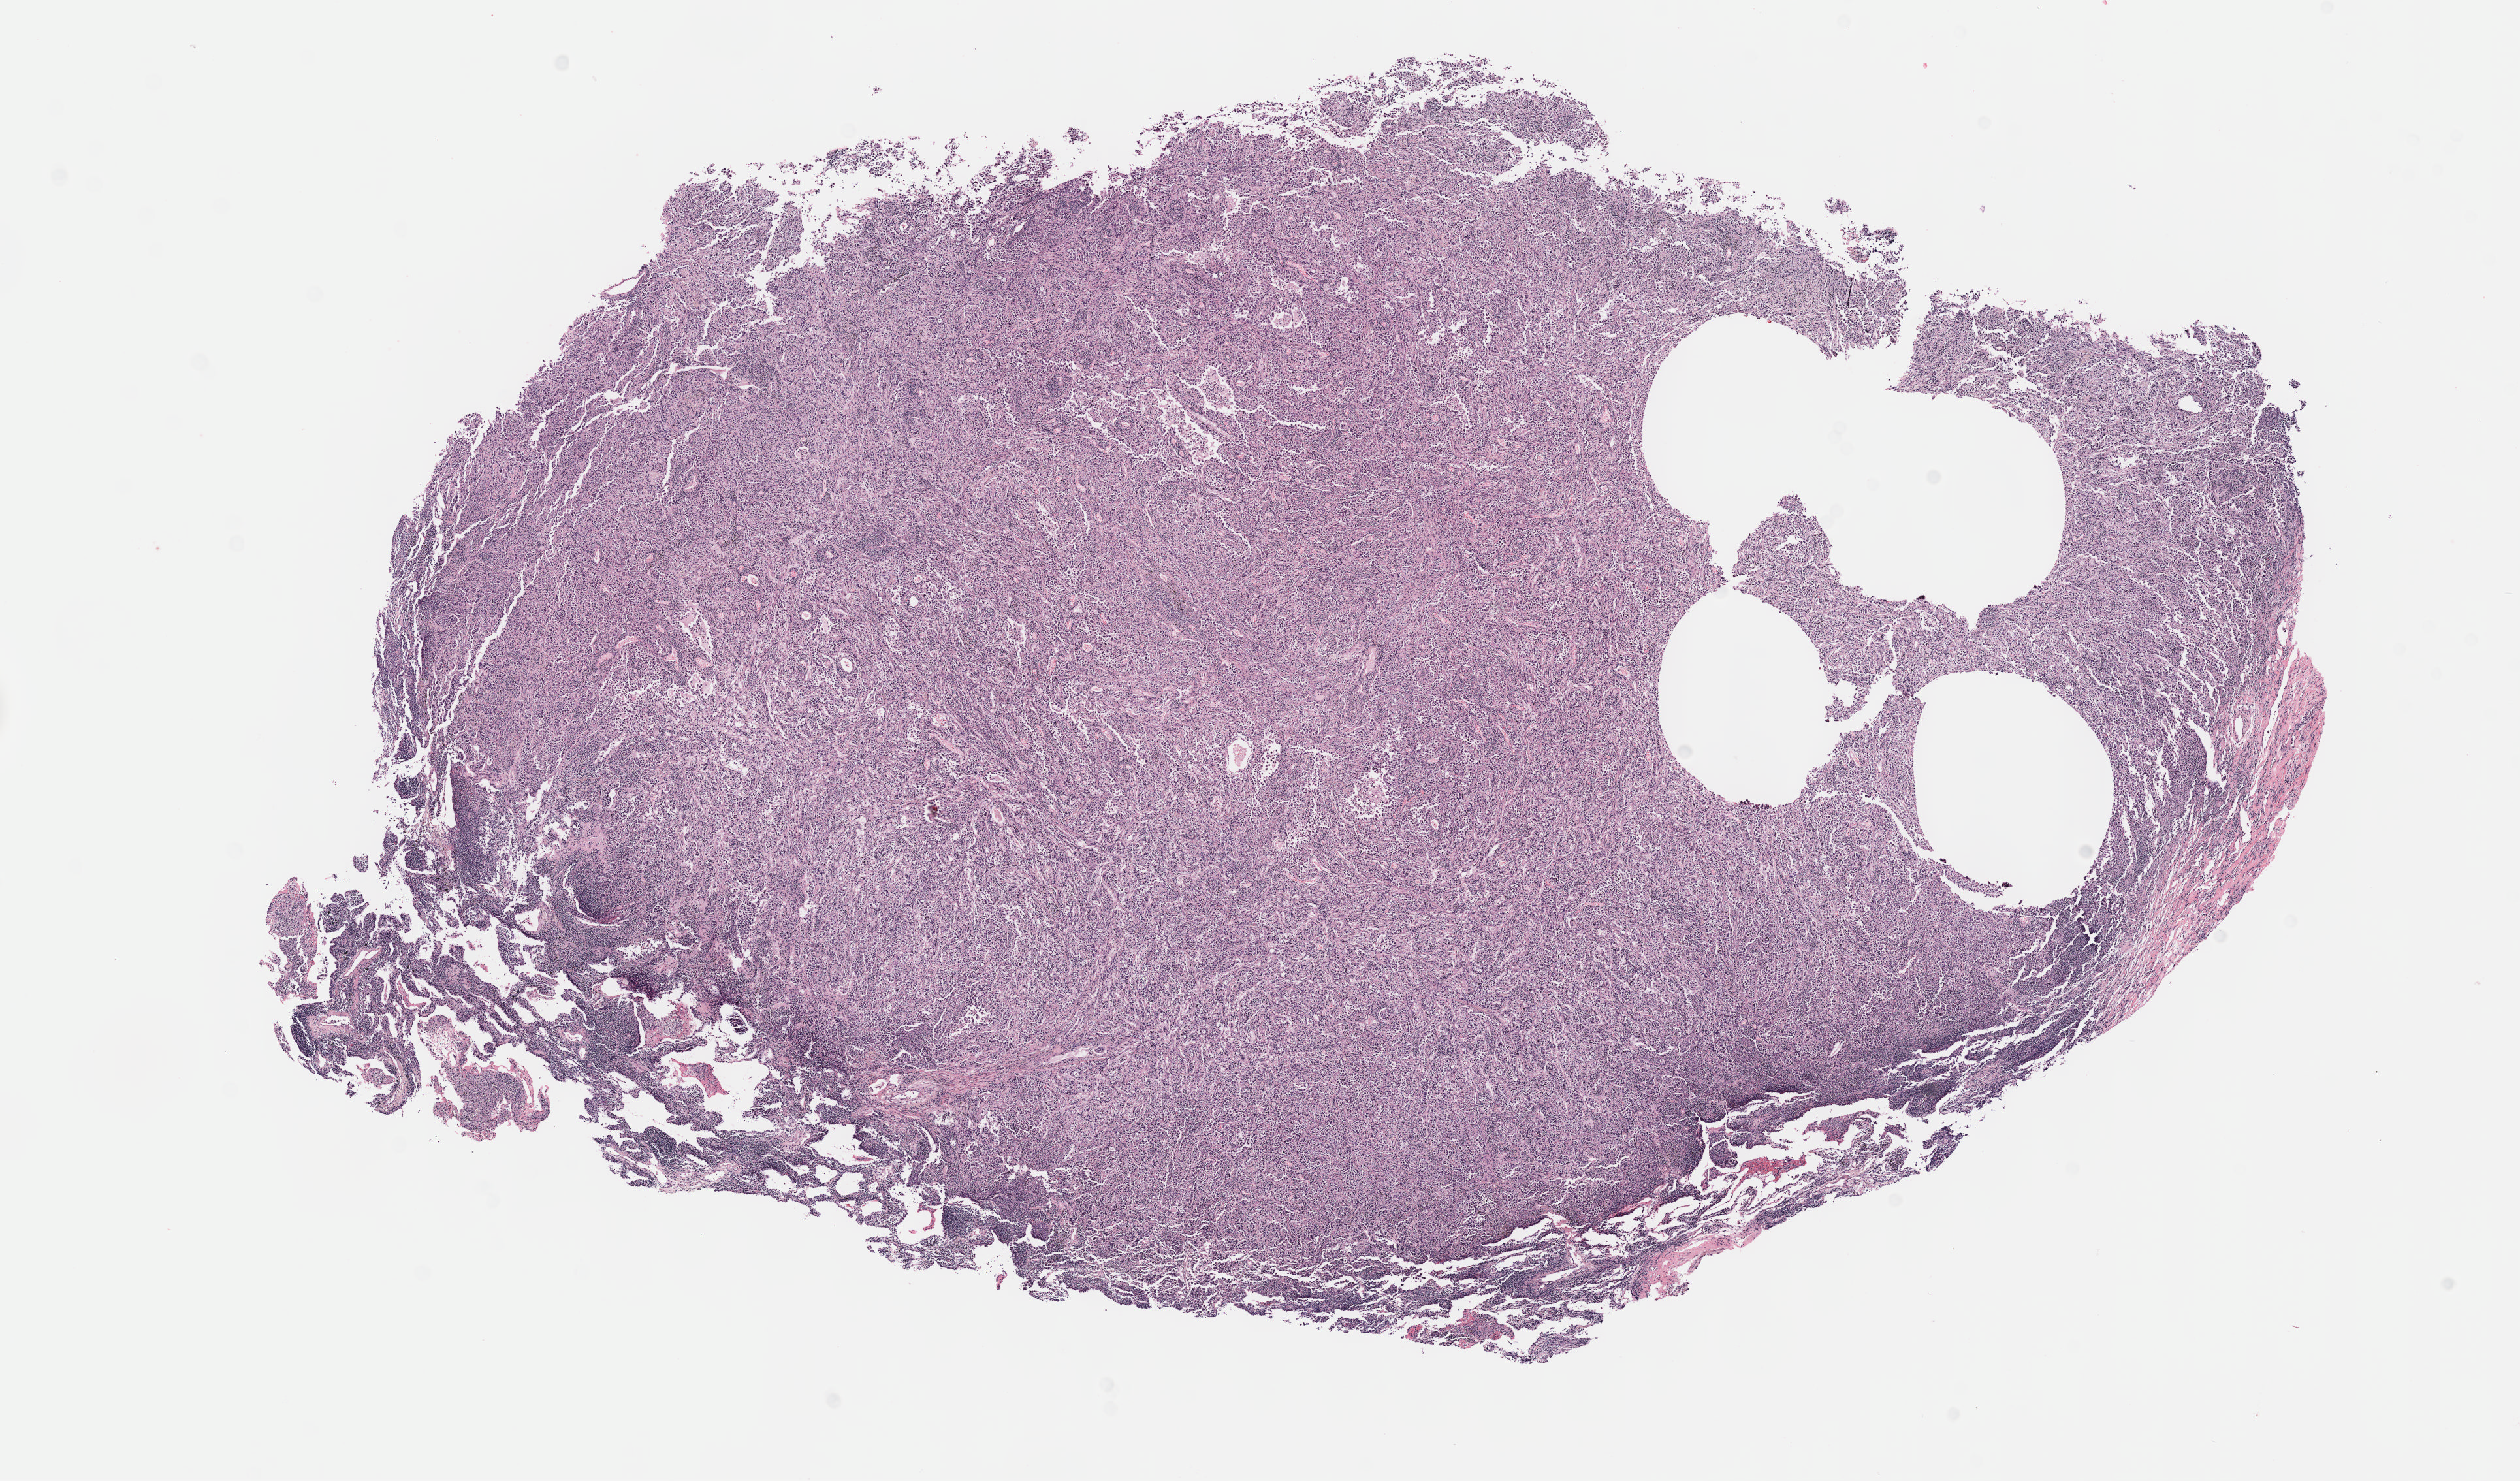
Whole-slide histology image, H&E-stained — low-resolution overview of the scanned area, about 15.6 x 9.2 mm (from a 40x scan), formalin-fixed paraffin-embedded (FFPE) diagnostic section, lung, primary tumour sample. Female patient; age at initial diagnosis 55 years.
• diagnosis: Adenocarcinoma with mixed subtypes (upper lobe, lung)
• AJCC pathologic stage: IB (6th edition)